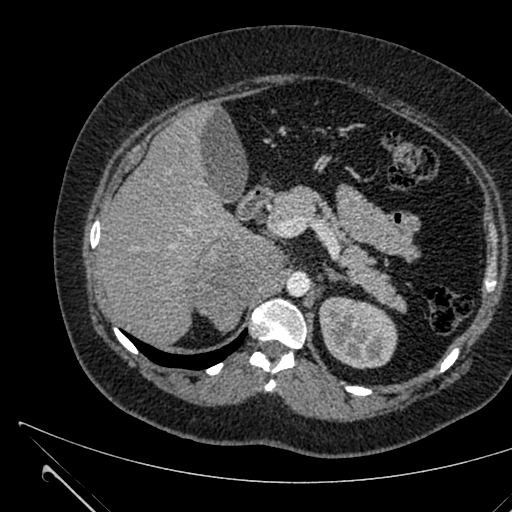
Contrast-enhanced abdominal CT, one axial slice. Position 428 of 731 along the scan axis. 120 kVp. Soft-tissue window (W 400 / L 40 HU). 512 × 512 image matrix, field of view 376 × 376 mm. Patient: female, 36 years. Case-level facts recorded for this patient, not image findings: diagnosis: adrenocortical carcinoma; tumour side: right adrenal; tumour size at pathology: 10 cm; Ki-67 index: 20 %; stage (as recorded): 4.
Outlined on this slice (semi-automatic segmentation, software-assisted and operator-edited):
- mass: bounding box [x1, y1, x2, y2] px = [189, 235, 284, 330]